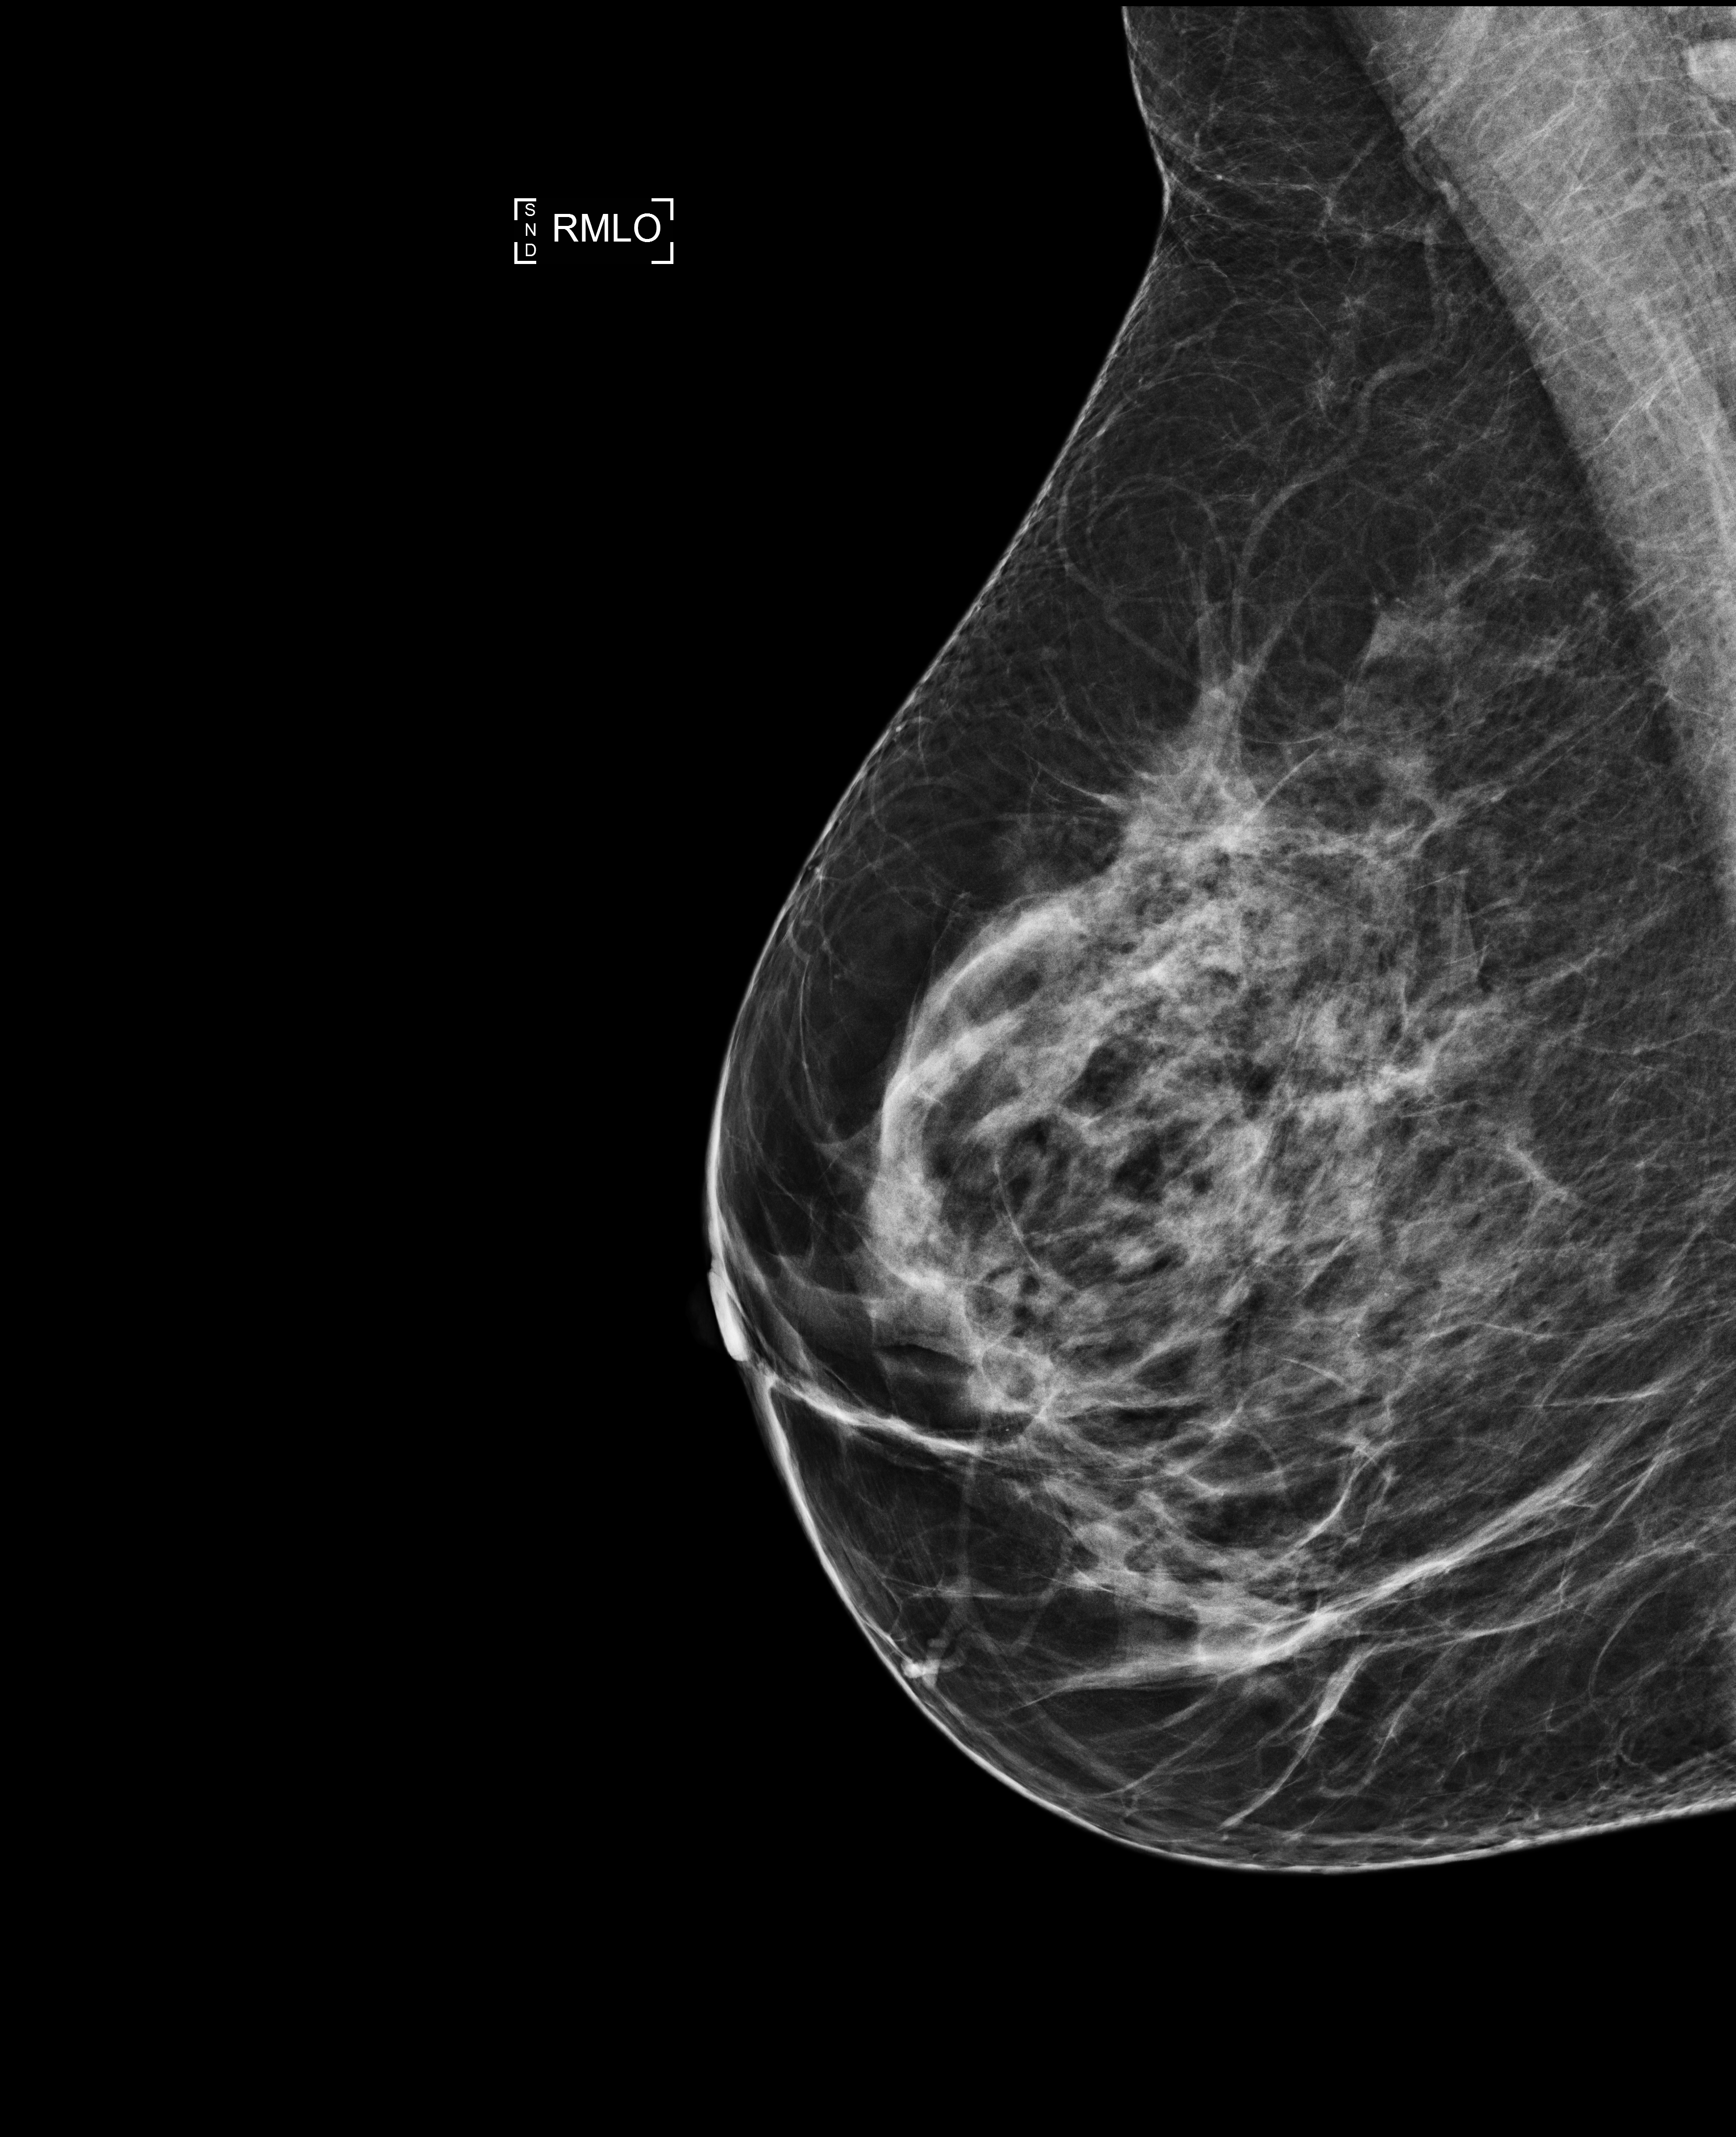
Screening examination. Female patient, age 54 years.
Image type: full-field digital mammogram. Breast: right. Projection: MLO view.